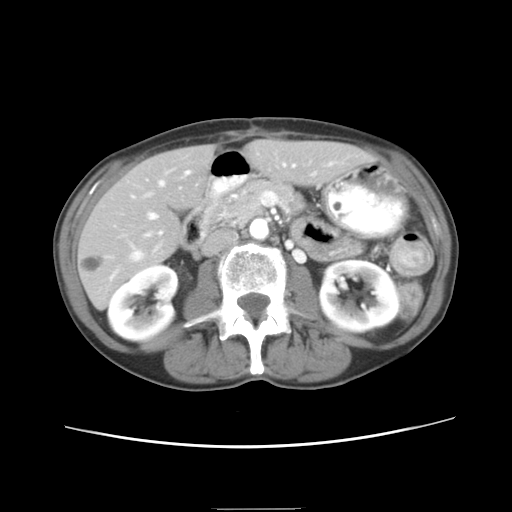
Contrast-enhanced abdominal CT, one axial slice; reconstruction kernel STANDARD; intravenous contrast given; soft-tissue window (W 400 / L 40 HU); 7.5 mm slice thickness; 512 × 512 image matrix, field of view 340 × 340 mm. Female patient, age 65 years. Case-level facts recorded for this patient, not image findings: diagnosis: colorectal cancer liver metastases, imaged before liver resection; multiple liver metastases: no; disease in both lobes: yes; chemotherapy before resection: yes.
Structures marked on this image (outlined manually by an expert reader):
- hepatic veins: bounding box [x1, y1, x2, y2] px = [131, 162, 310, 260]
- liver: [78, 141, 367, 304]
- planned liver remnant (the part of the liver to remain after resection): [82, 141, 367, 304]
- portal vein (with intrahepatic branches): [131, 163, 315, 236]
- liver metastasis: [79, 255, 105, 274]